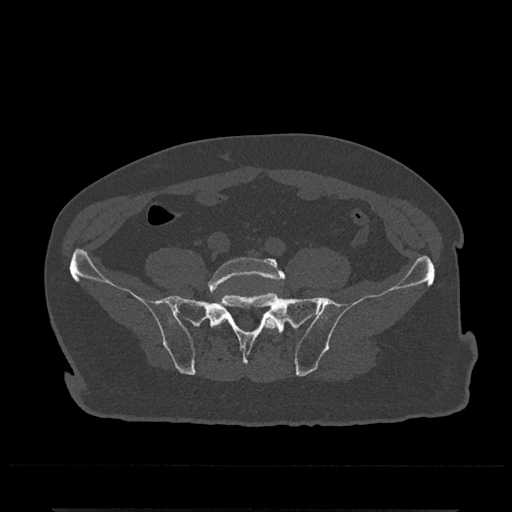
CT including the spine, one axial slice; position 48 of 797 along the scan axis; 120 kVp; bone window (W 1800 / L 400 HU); 512 × 512 image matrix, field of view 393 × 393 mm. Patient: male, 67 years. From the clinical record (not read from this slice): primary cancer: prostate.
Annotated regions visible in this slice (semi-automatic segmentation, software-assisted and operator-edited):
- L5 vertebra: bounding box [x1, y1, x2, y2] px = [208, 257, 285, 330]